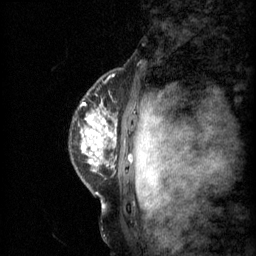
Breast MRI (dynamic contrast-enhanced), one sagittal slice. Slice 49 of 60 in the series (ordered by position). 3 images stored at this slice position (order not interpretable as contrast timing). 1.5 T. TE 4.2 ms, TR 11 ms. 2 mm slice thickness. 256 × 256 image matrix, field of view 200 × 200 mm. Female patient, age 48 years.
Outlined on this slice (semi-automatic segmentation, software-assisted and operator-edited):
- analysis volume of interest (the breast-tissue region the enhancement analysis was run in; not a lesion): bounding box (x1, y1, x2, y2) in pixels: (80, 94, 138, 147)
- tumour enhancement mask (voxels above the 70 % enhancement threshold inside the analysis volume of interest): (83, 116, 117, 147)